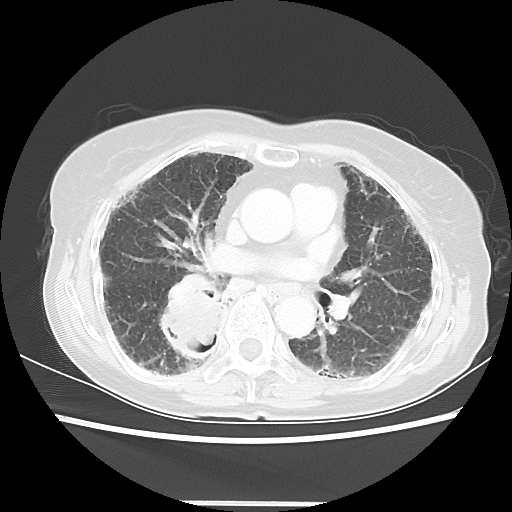
Chest CT, one axial slice; slice 28 of 52 in the series (ordered by position); reconstruction kernel LUNG; 120 kVp; lung window (W 1500 / L -600 HU); 512 × 512 image matrix, field of view 325 × 325 mm. Female patient, age 71 years. From the clinical record (not read from this slice): clinical TNM (as recorded): T3 N0 M0.
Outlined on this slice (bounding box drawn by a radiologist):
- lung tumour (recorded histology: squamous cell carcinoma): bounding box <157,277,223,363> (left, top, right, bottom; pixels)